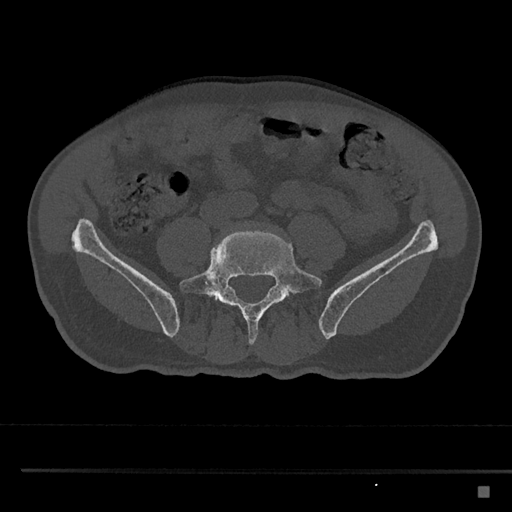
CT including the spine, one axial slice. Slice 586 of 797 in the series (ordered by position). 120 kVp. Bone window (W 1800 / L 400 HU). 0.5 mm slice thickness. 512 × 512 image matrix, field of view 391 × 391 mm. Male patient, age 59 years. From the clinical record (not read from this slice): primary cancer: prostate.
Annotated regions visible in this slice (semi-automatic segmentation, software-assisted and operator-edited):
- L5 vertebra: bounding box [x1, y1, x2, y2] px = [179, 229, 322, 345]